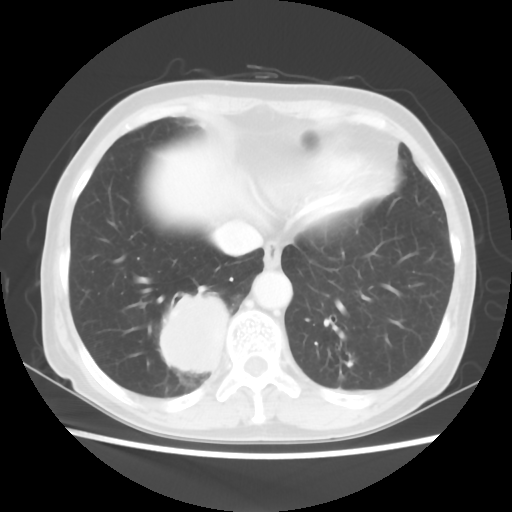
Chest CT, one axial slice. Slice 15 of 56 in the series (ordered by position). Reconstruction kernel STANDARD. 120 kVp. Lung window (W 1500 / L -600 HU). 5 mm slice thickness. 512 × 512 image matrix. Patient: female, 66 years. From the clinical record (not read from this slice): clinical TNM (as recorded): T2 N3 M0; histopathological grade: G3.
Outlined on this slice (rectangle marked by the reading radiologist):
- lung tumour (recorded histology: small cell carcinoma): bounding box <153,292,232,387> (left, top, right, bottom; pixels)